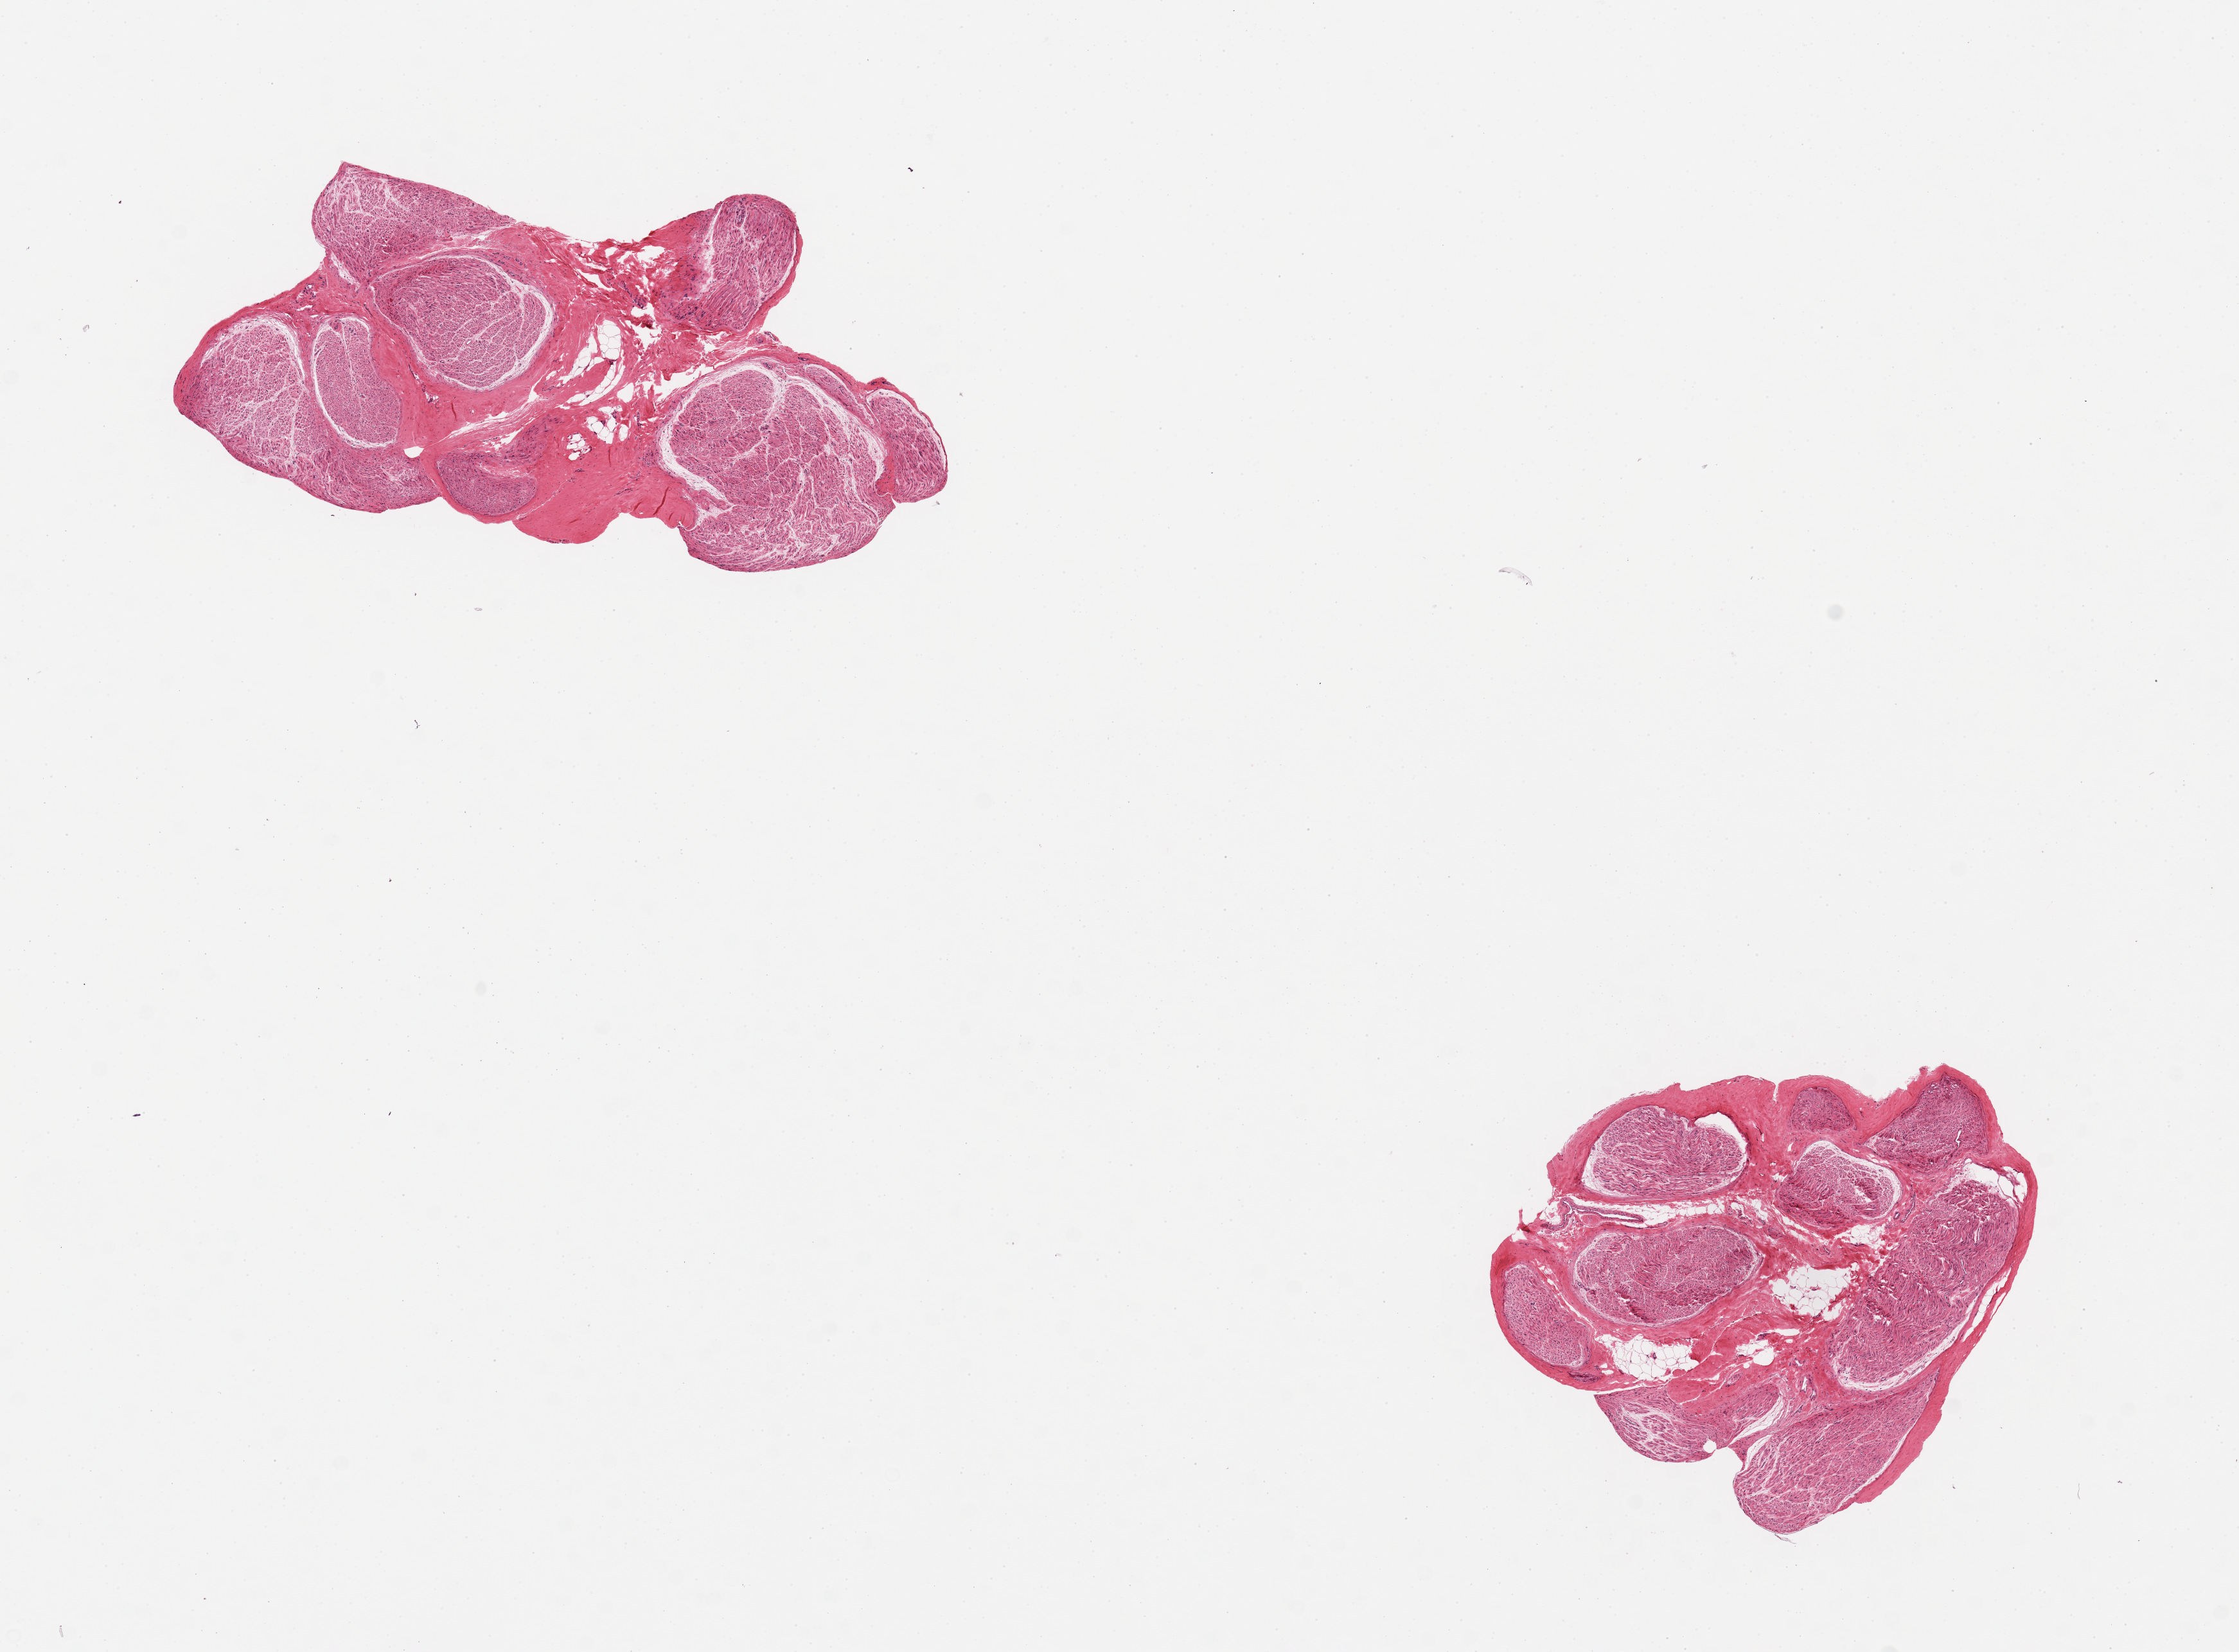
Whole-slide image, haematoxylin and eosin stain, brightfield — shown as a low-resolution overview of the whole scanned area (about 13.8 x 10.2 mm, acquisition: 20x scan). PAXgene-fixed, paraffin-embedded tissue. Target tissue: tibial nerve. Donor tissue sample. Male donor.
Pathologist's review note for this sample: 2 pieces, no adherent fat, good specimens.